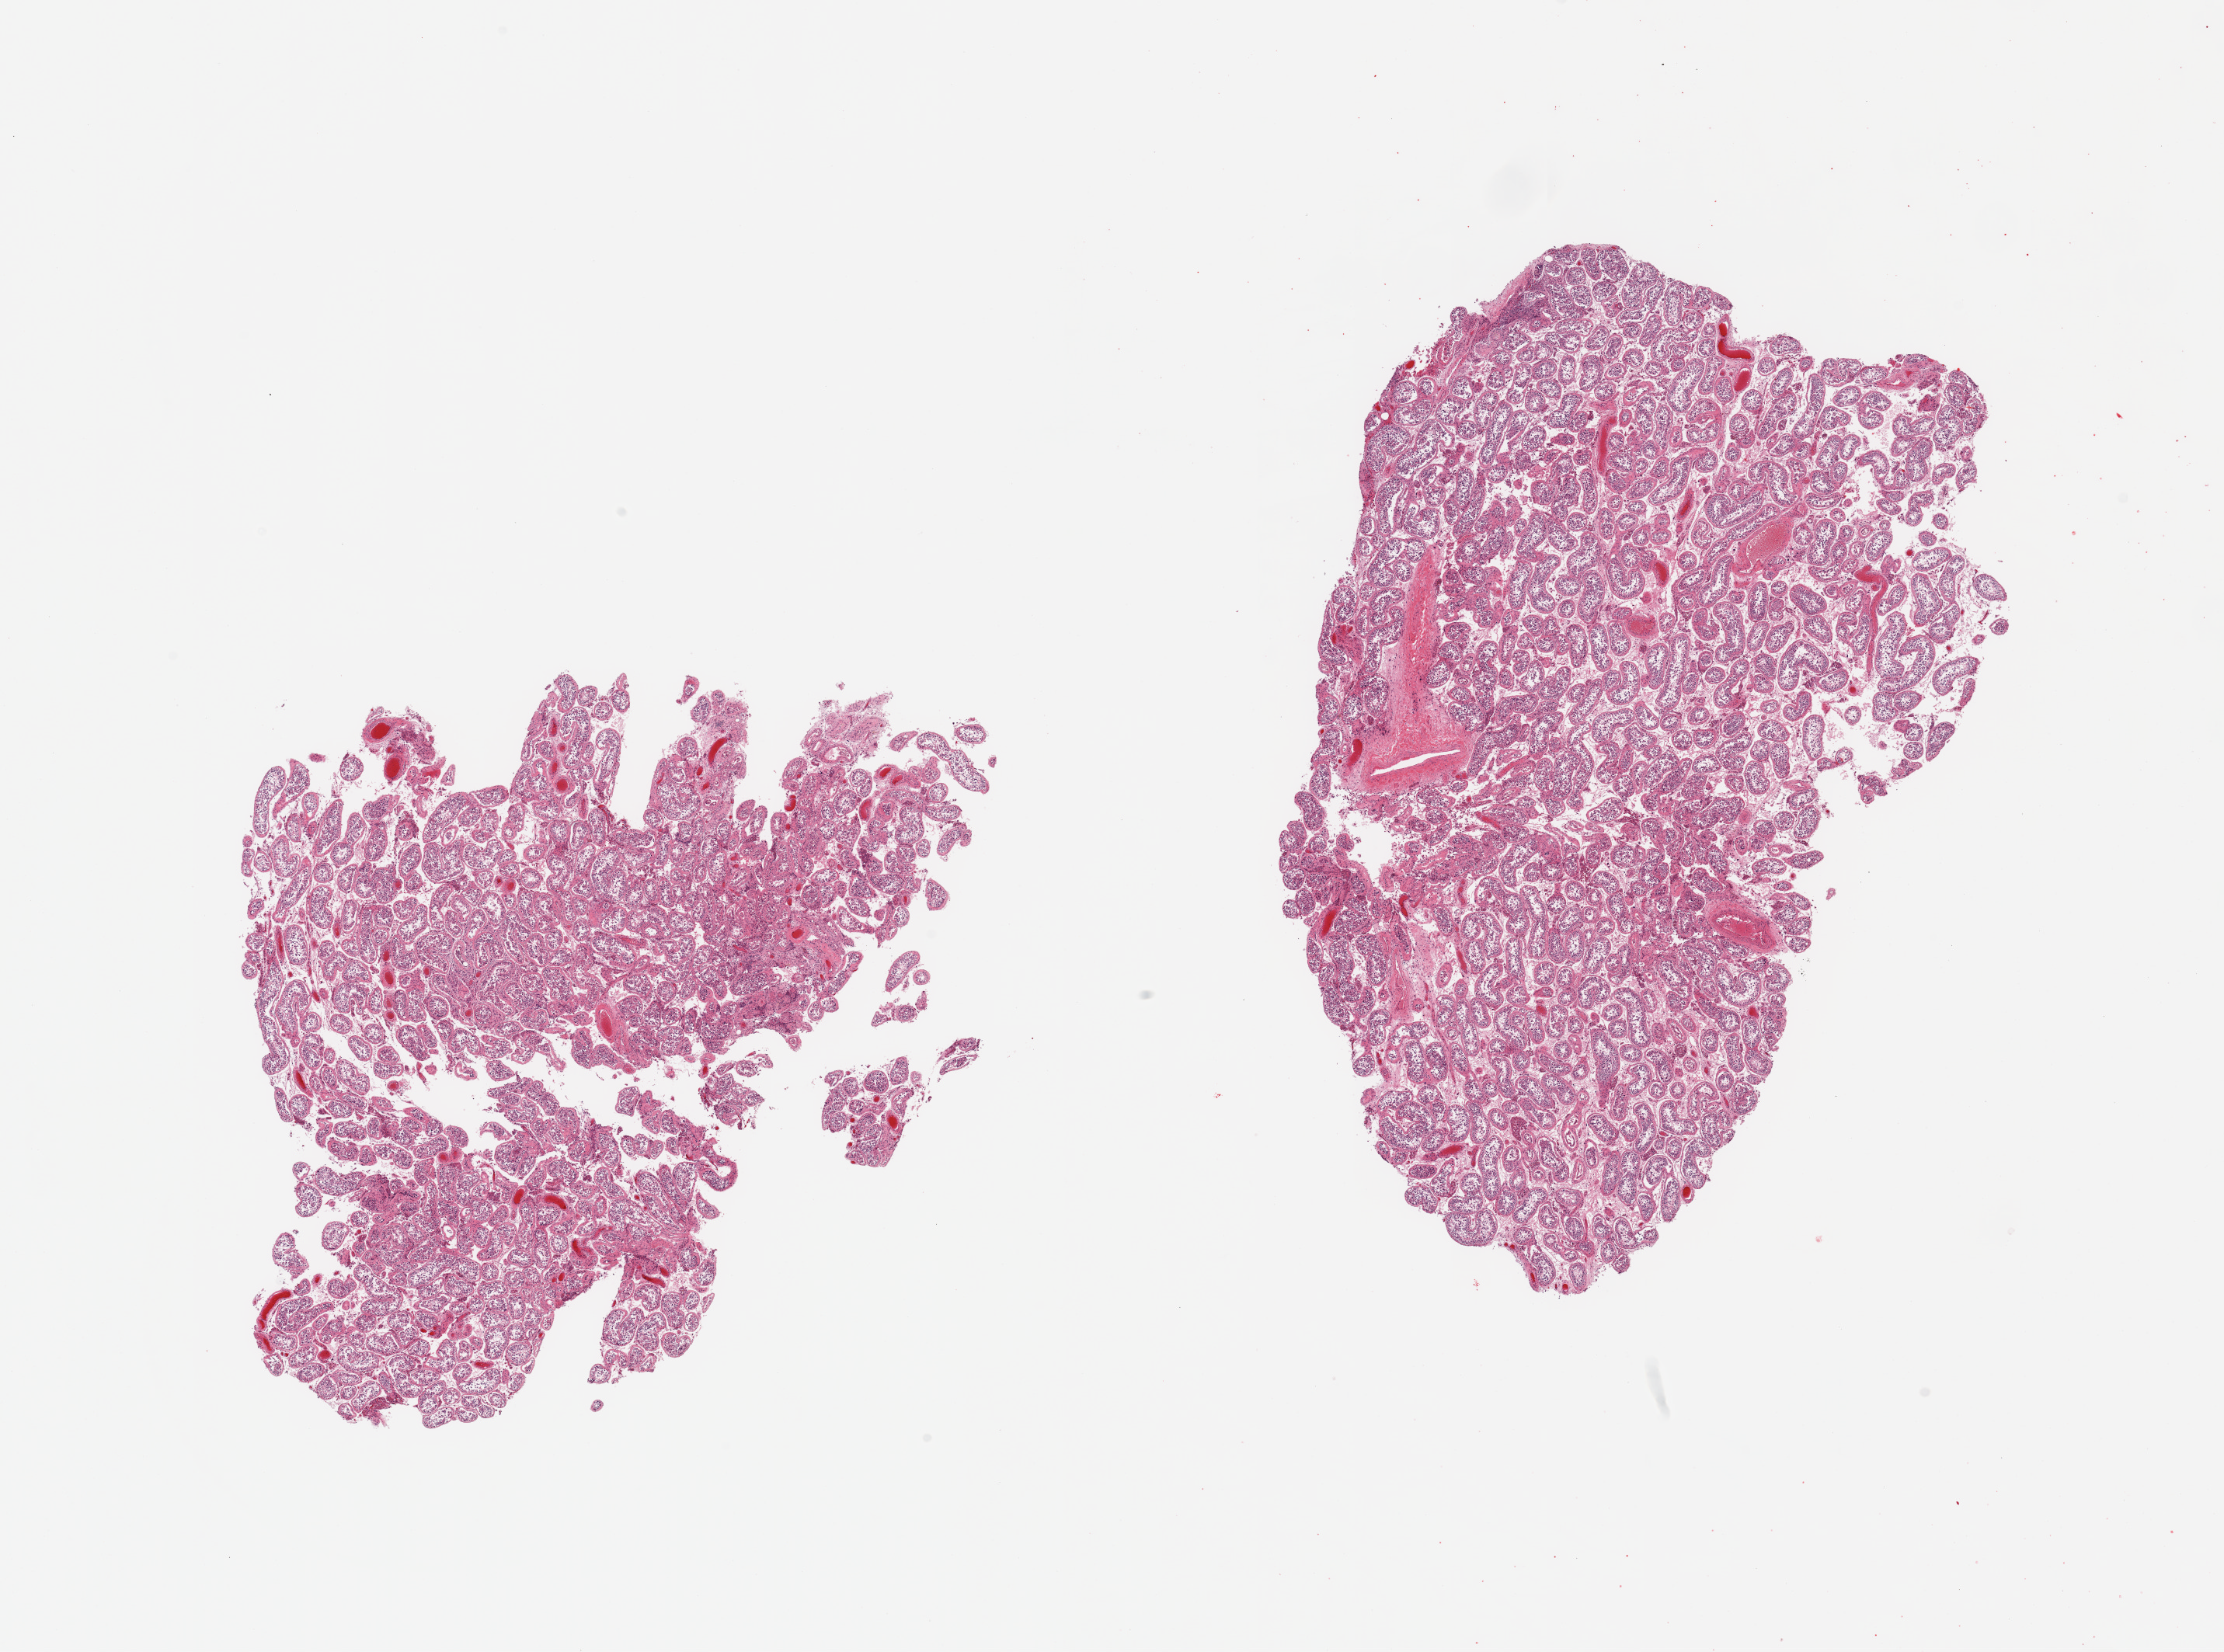
Hematoxylin and eosin (H&E) whole-slide image, brightfield — shown as a low-resolution overview of the whole scanned area (about 22.6 x 16.8 mm), PAXgene-fixed, paraffin-embedded tissue, sampled site (target tissue): testis, tissue donor sample. Male donor.
Pathologist's review note for this sample: 2 pieces, spermatogenesis appears slightly reduced.